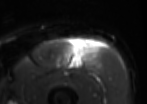
MRI of an extremity soft-tissue mass, one axial slice. Position 38 of 85 along the scan axis. T2-weighted fat-saturated. MR volume resampled by the dataset authors to the PET/CT grid (not the native acquisition matrix). 3.27 mm slice thickness. 147 × 104 image matrix, field of view 144 × 102 mm. Male patient. Case-level facts recorded for this patient, not image findings: histological type: extraskeletal osteosarcoma; grade: high; site of the primary tumour: thigh.
Annotated regions visible in this slice (expert contour drawn on MRI and transferred to this co-registered scan by the dataset authors):
- gross tumour volume (mass): bounding box <67,40,89,68> (left, top, right, bottom; pixels)